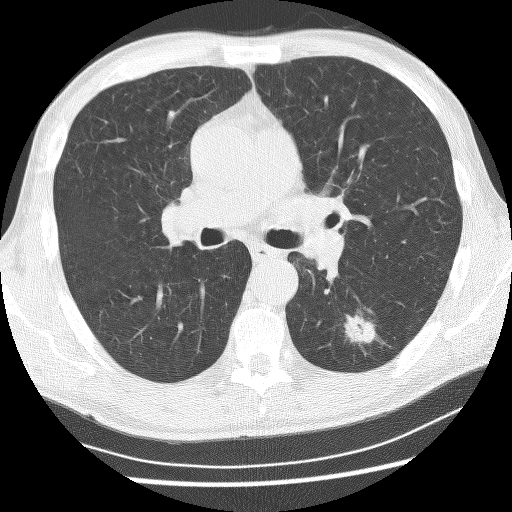
Chest CT (low-dose screening protocol), one axial image. Baseline screening round. Lung window (W 1500 / L -600 HU). 2.5 mm slice thickness. Lung (sharp) reconstruction kernel (BONE). Slice 106 of 253 in the series. Male participant, aged 62 years at enrolment. Current smoker at enrolment.
- Lesion marked by an expert reader, bounding box (x1, y1, x2, y2) in pixels: (331, 308, 382, 353).
- The exam's reader record, not a measurement of the box and not confirmed to be the same lesion: non-calcified nodule or mass ≥4 mm, left lower lobe, 21 × 17 mm, spiculated (stellate) margins, soft tissue attenuation.
- Official screen result: positive, change unspecified: nodule(s) >= 4 mm or enlarging nodule(s), mass(es), or other non-specific abnormalities suspicious for lung cancer.
- Later outcome: lung cancer diagnosed 58 days after this screen — non-small cell carcinoma, left lower lobe, poorly differentiated (G3), stage IA (AJCC 6th edition), 11 mm at pathology.